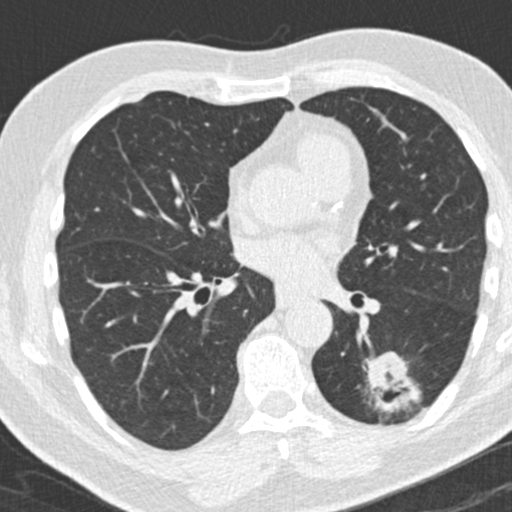
Low-dose screening chest CT, one axial slice. Slice 96 of 180 in the series (ordered by position). Reconstruction kernel B30f. 120 kVp. Lung window (W 1500 / L -600 HU). 512 × 512 image matrix, field of view 300 × 300 mm.
Structures marked on this image (expert manual segmentation):
- lesion 1 (tumor, lower lobe of left lung): bounding box [x1, y1, x2, y2] px = [368, 353, 406, 390]